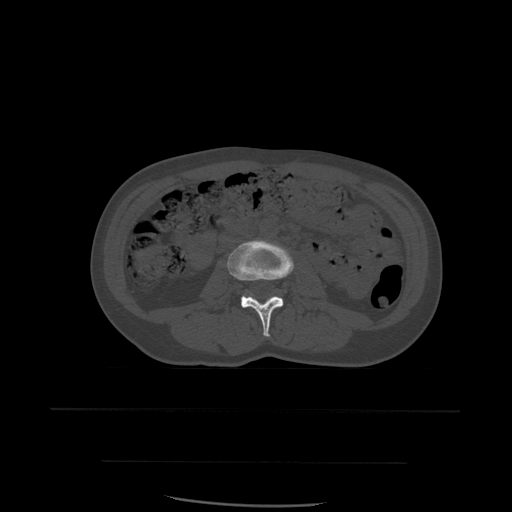
CT including the spine, one axial slice. Position 192 of 574 along the scan axis. Bone window (W 1800 / L 400 HU). 1.25 mm slice thickness. 512 × 512 image matrix, field of view 392 × 392 mm. Patient age 48 years. From the clinical record (not read from this slice): primary cancer: lung; vertebrae with lytic lesions (as recorded): T11.
Outlined on this slice (semi-automatically segmented with operator editing):
- L3 vertebra: bounding box (x1, y1, x2, y2) in pixels: (227, 240, 294, 337)